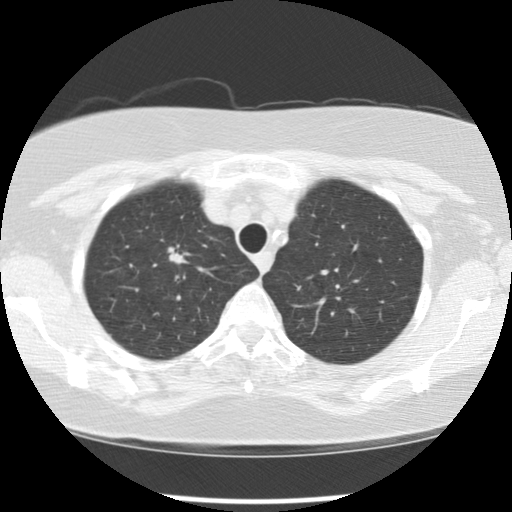
Low-dose screening chest CT, one axial slice; position 93 of 113 along the scan axis; lung window (W 1500 / L -600 HU); 2.5 mm slice thickness; 512 × 512 image matrix, field of view 318 × 318 mm.
Annotated regions visible in this slice (expert manual segmentation):
- lesion 1 (tumor, upper lobe of right lung): bounding box <168,247,190,264> (left, top, right, bottom; pixels)